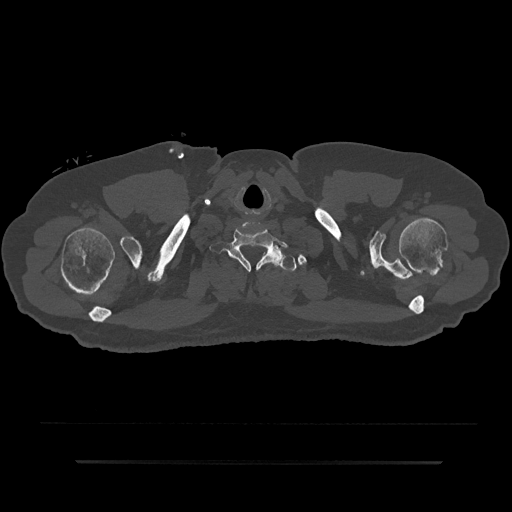
CT including the spine, one axial slice; slice 766 of 797 in the series (ordered by position); bone window (W 1800 / L 400 HU); 512 × 512 image matrix, field of view 464 × 464 mm. Male patient, age 59 years. From the clinical record (not read from this slice): primary cancer: bile ducts; vertebrae with lytic lesions (as recorded): T10.
Outlined on this slice (semi-automatically segmented with operator editing):
- T1 vertebra: bounding box <272,250,297,271> (left, top, right, bottom; pixels)